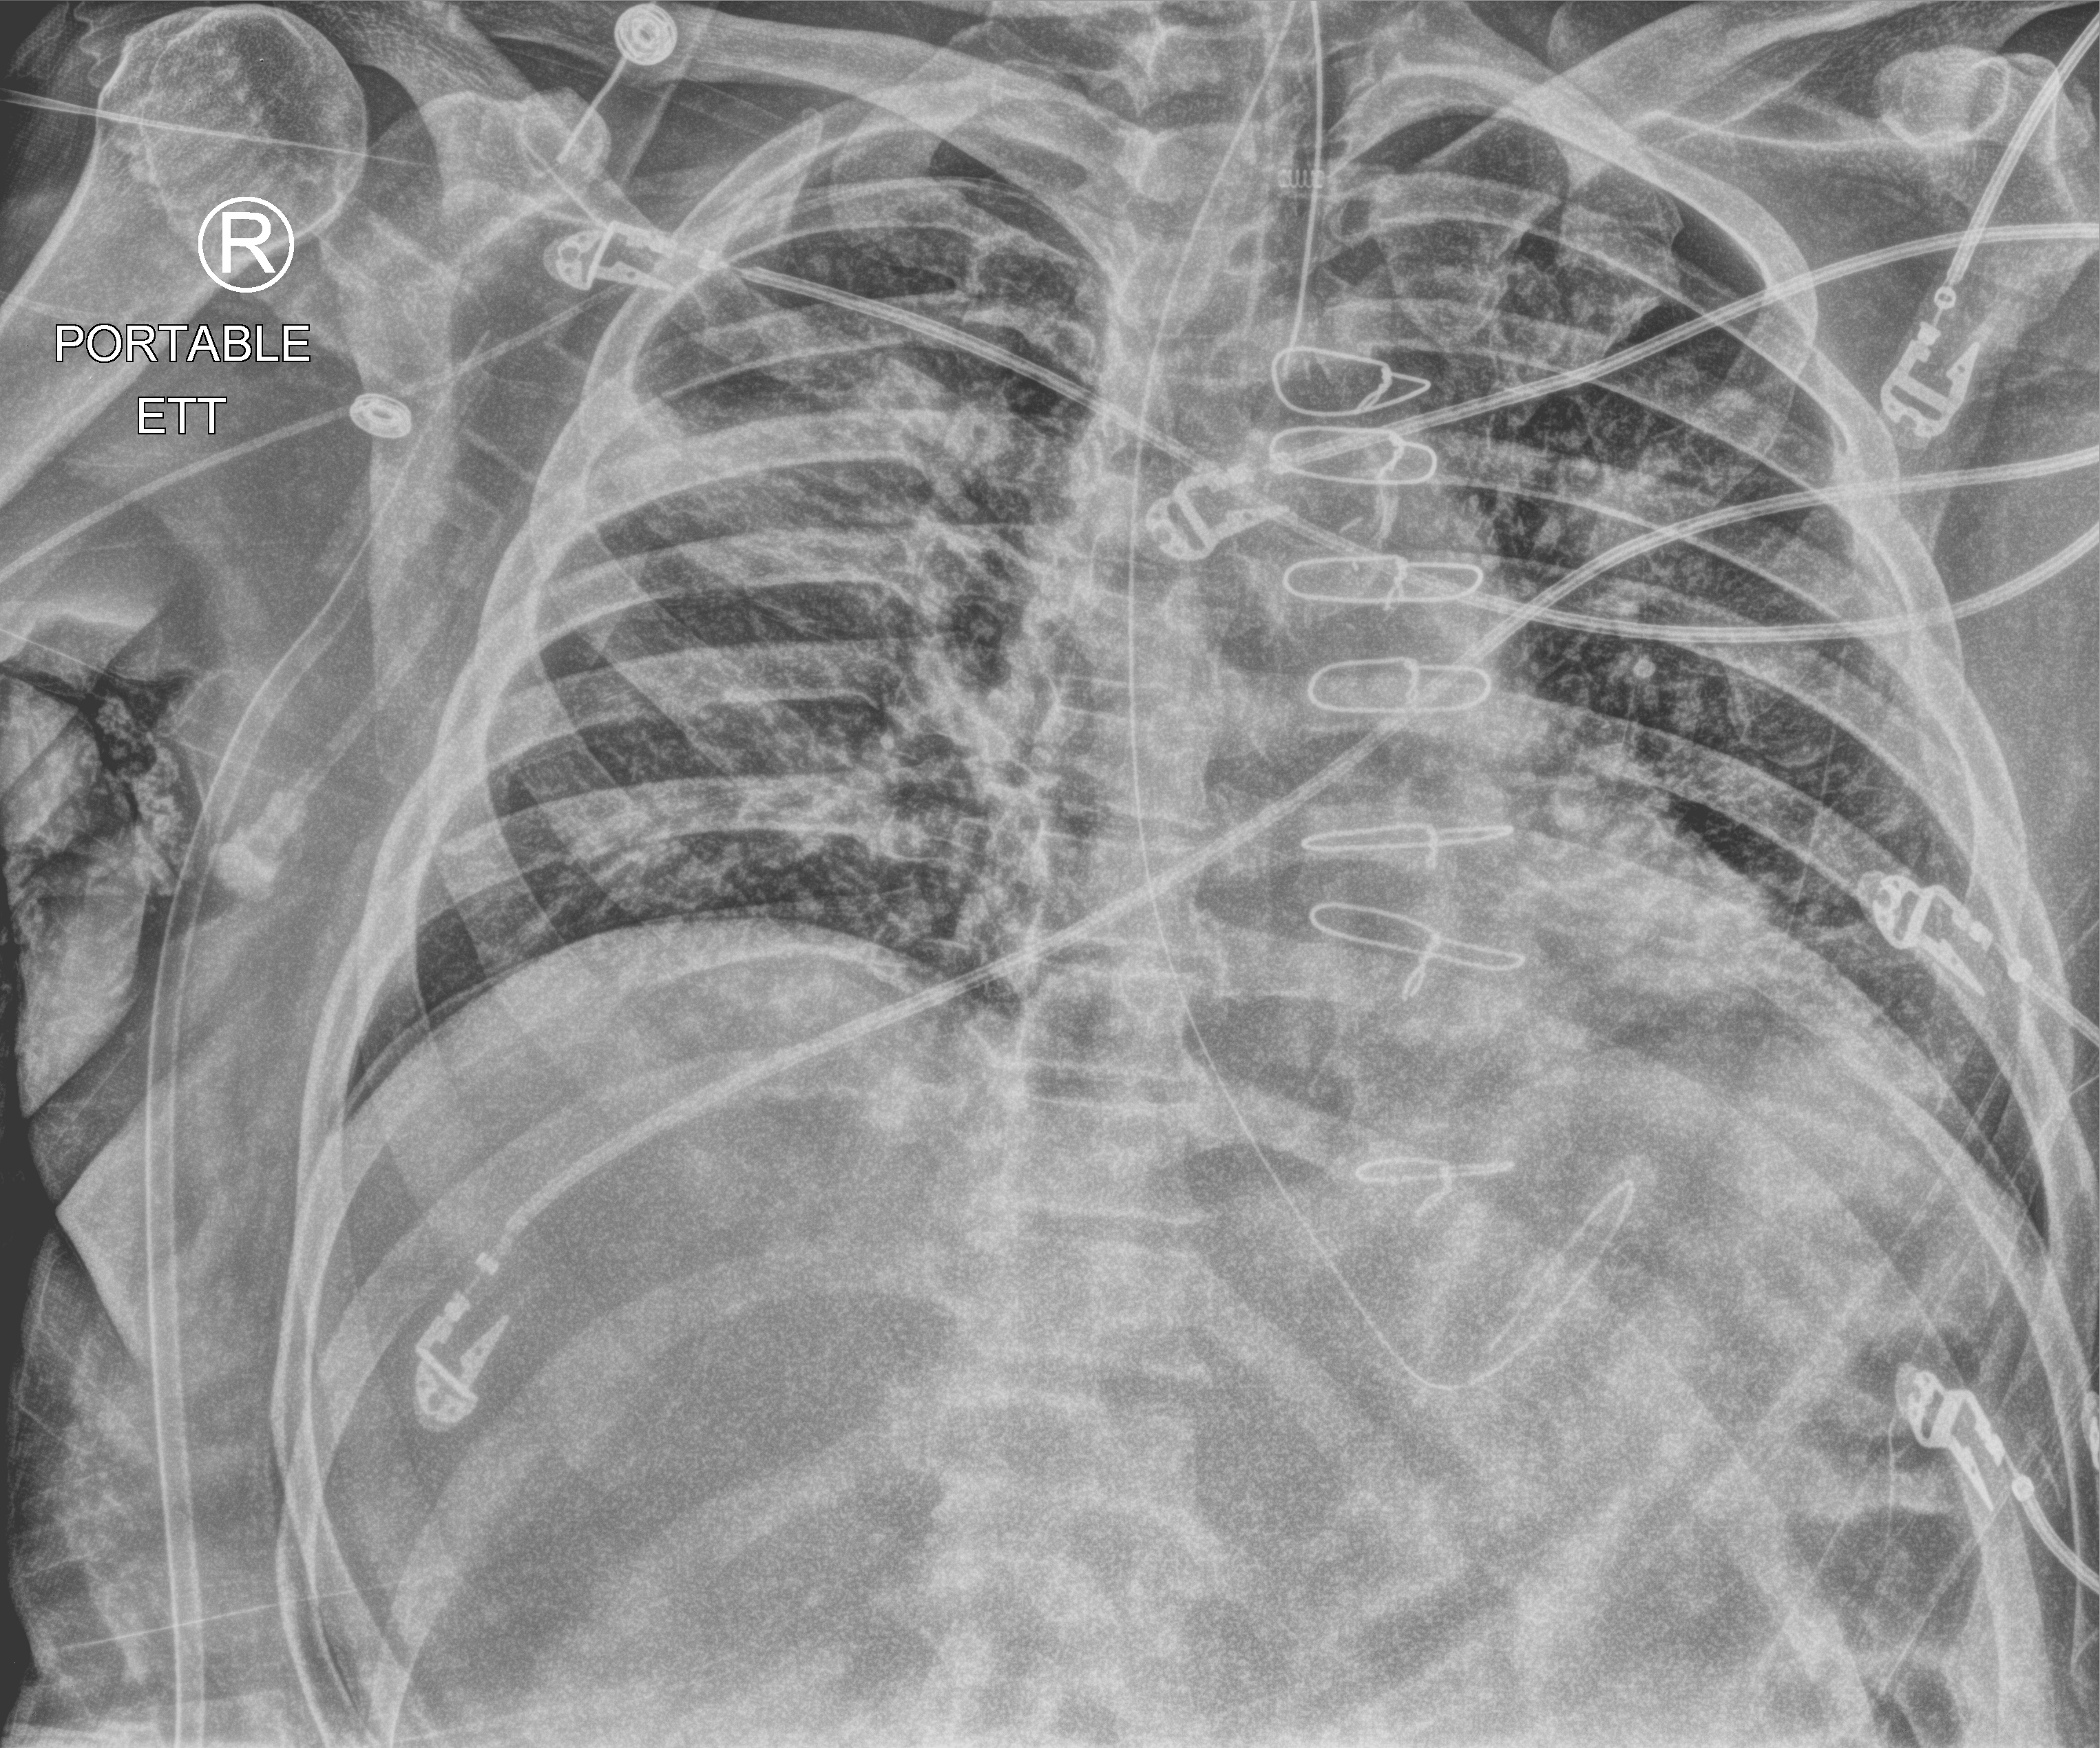
Chest X-ray (portable), anteroposterior (AP) projection. Patient hospitalised with COVID-19; male, aged 60–74 years.
From the hospital-stay record, not from the radiograph (when in the stay this image was taken is not recorded): mechanically ventilated during this hospital stay: yes.